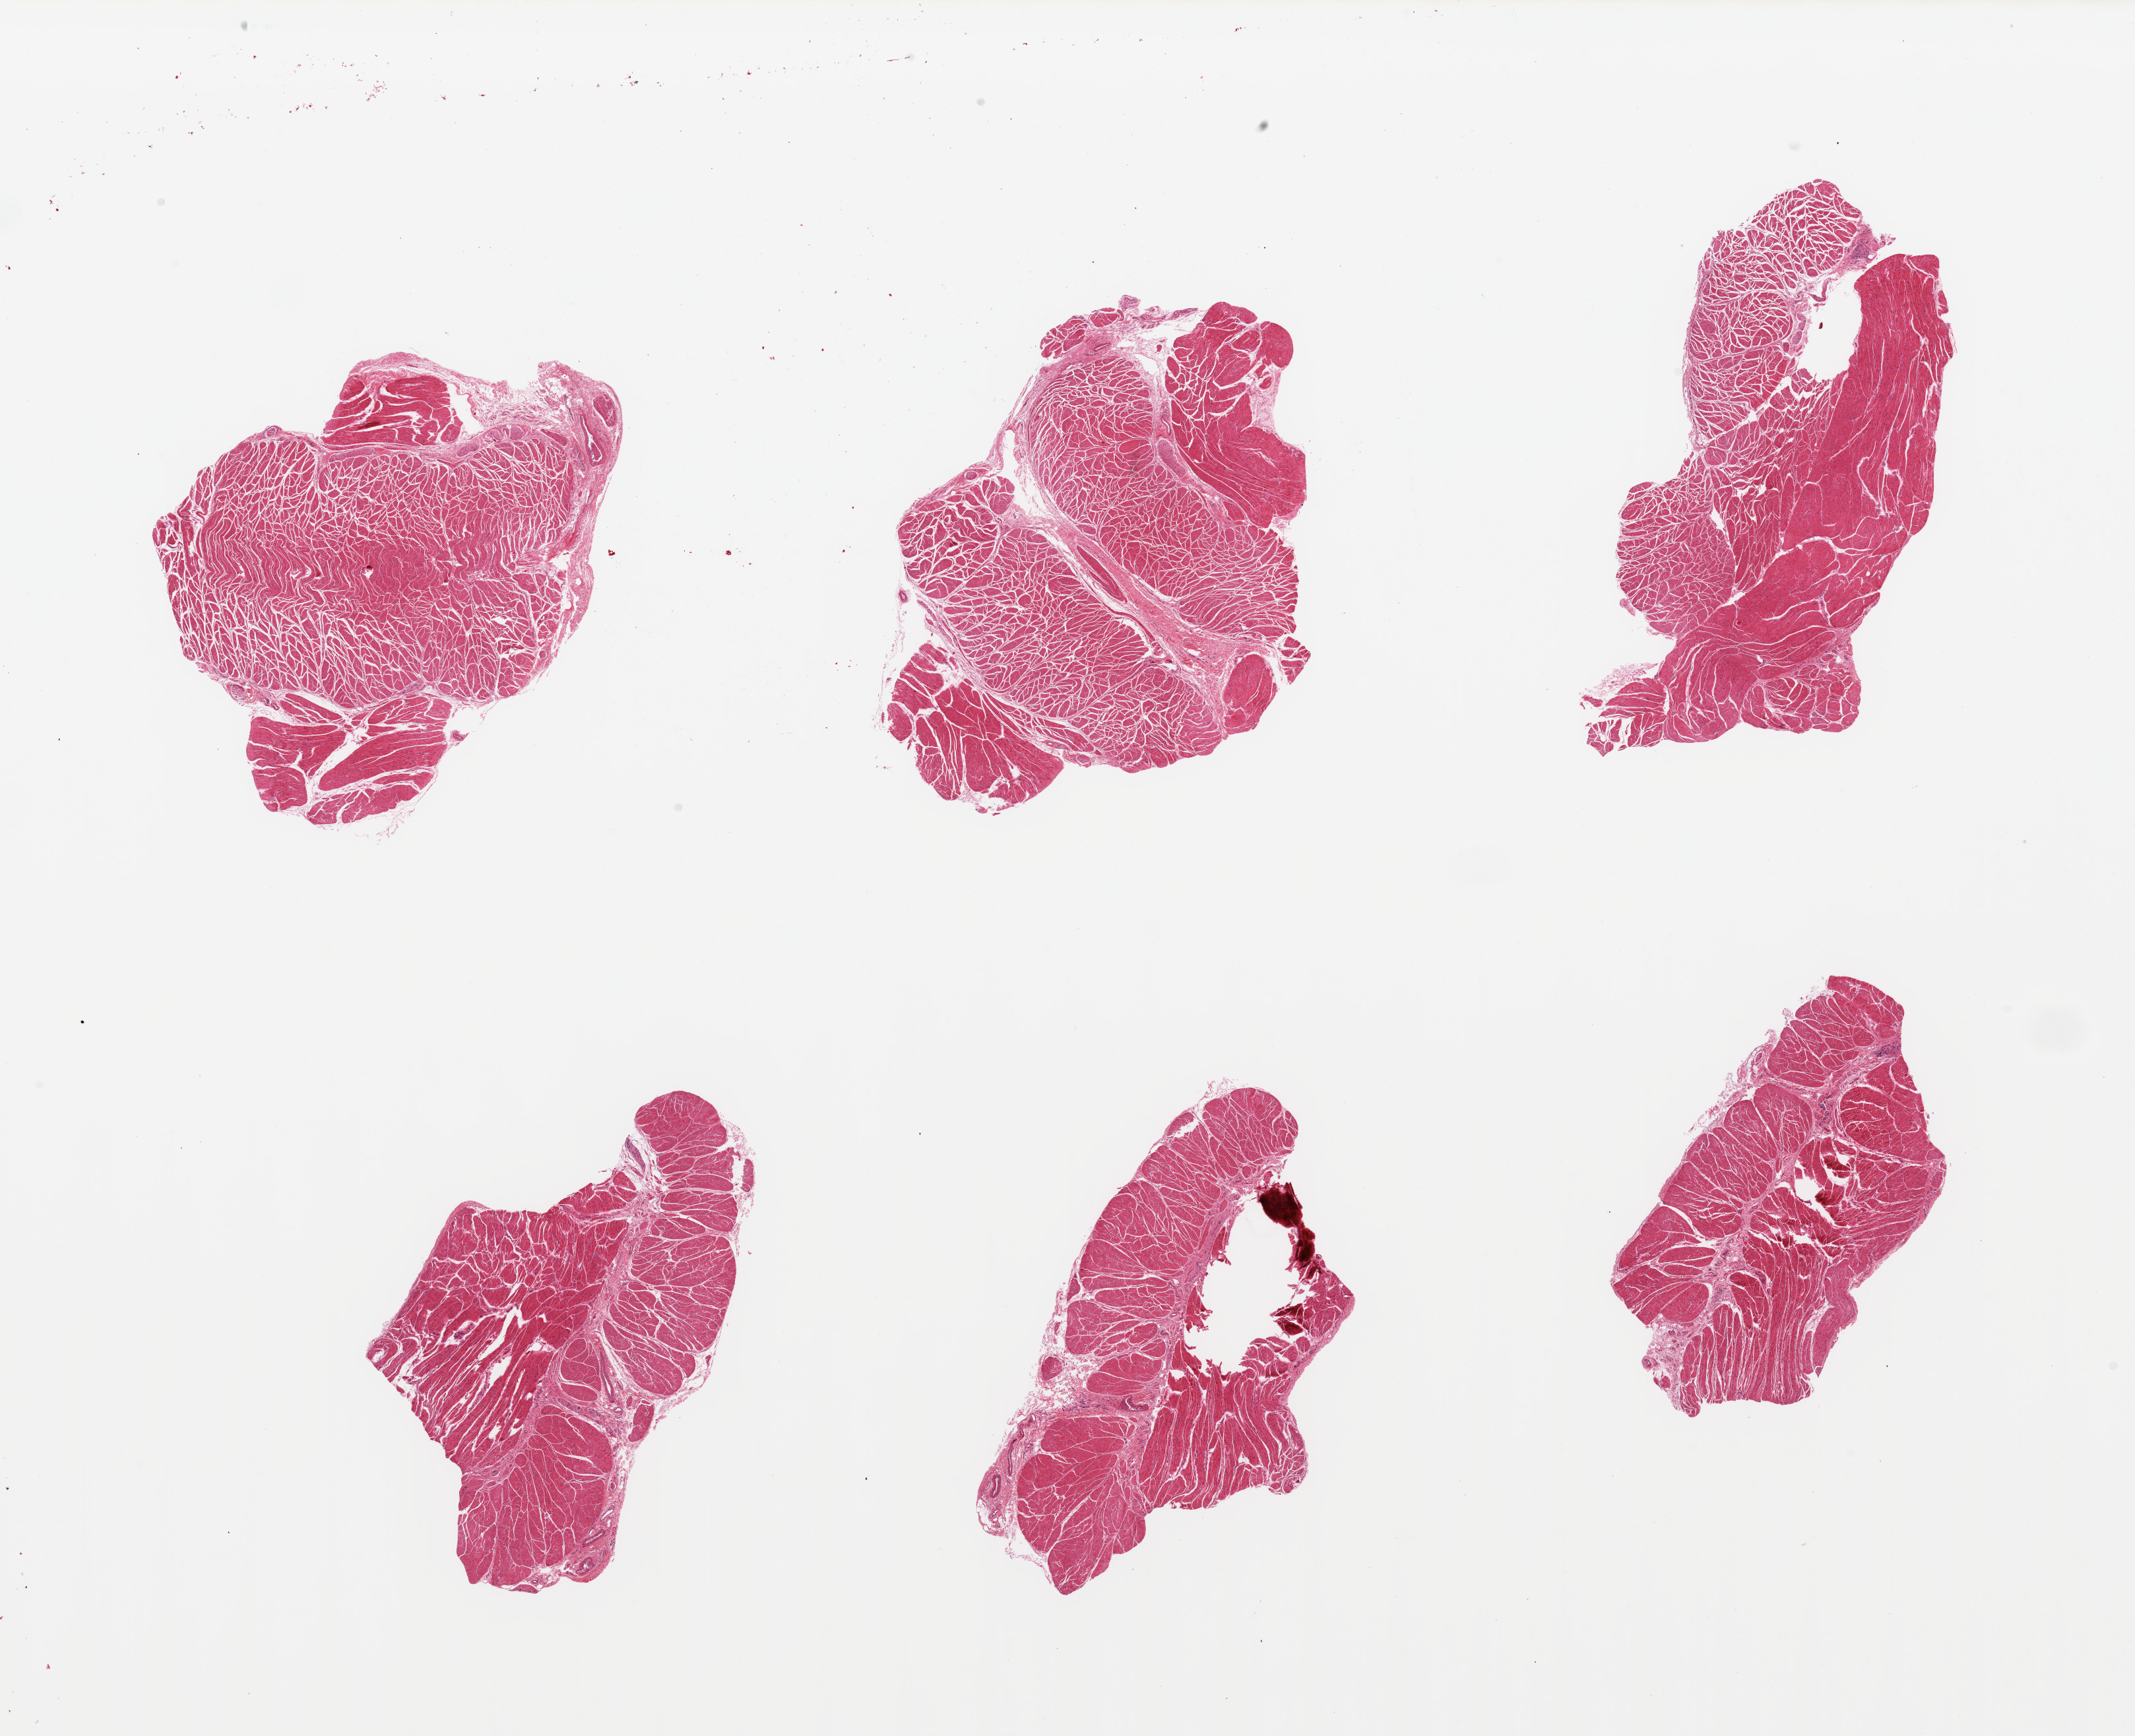
Whole-slide image, haematoxylin and eosin stain, brightfield — whole scanned area (about 25.6 x 20.8 mm) shown as a low-resolution overview; PAXgene-fixed paraffin-embedded (PFPE) section; sampled site (target tissue): esophageal muscle; donor tissue sample.
- review note (as recorded): 6 pieces; well dissected muscularis